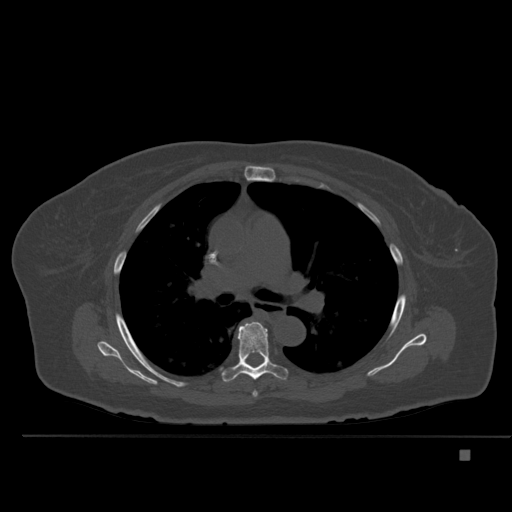
CT including the spine, one axial slice; position 341 of 477 along the scan axis; bone window (W 1800 / L 400 HU); 1.5 mm slice thickness; 512 × 512 image matrix. Patient: female, 74 years. Case-level facts recorded for this patient, not image findings: primary cancer: colon.
Annotated regions visible in this slice (semi-automatically segmented with operator editing):
- T5 vertebra: bounding box <252,391,258,397> (left, top, right, bottom; pixels)
- T6 vertebra: <222,321,287,382>